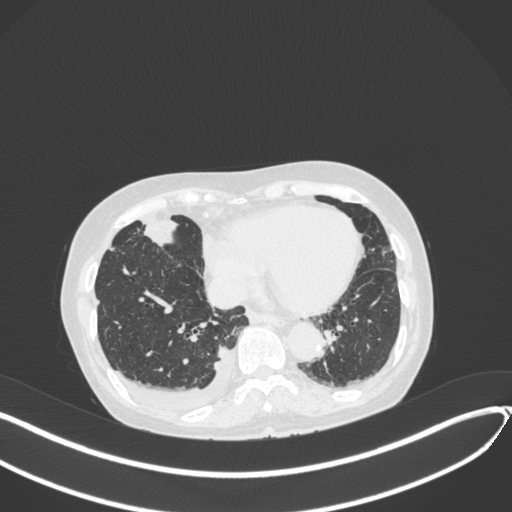
Chest CT, one axial slice. Slice 118 of 418 in the series (ordered by position). 120 kVp. Lung window (W 1500 / L -600 HU). 1 mm slice thickness. 512 × 512 image matrix. Female patient, age 75 years. Case-level facts recorded for this patient, not image findings: clinical TNM (as recorded): T2a N3 M0.
Outlined on this slice (bounding box drawn by a radiologist):
- lung tumour (recorded histology: adenocarcinoma): bounding box (x1, y1, x2, y2) in pixels: (138, 217, 183, 252)